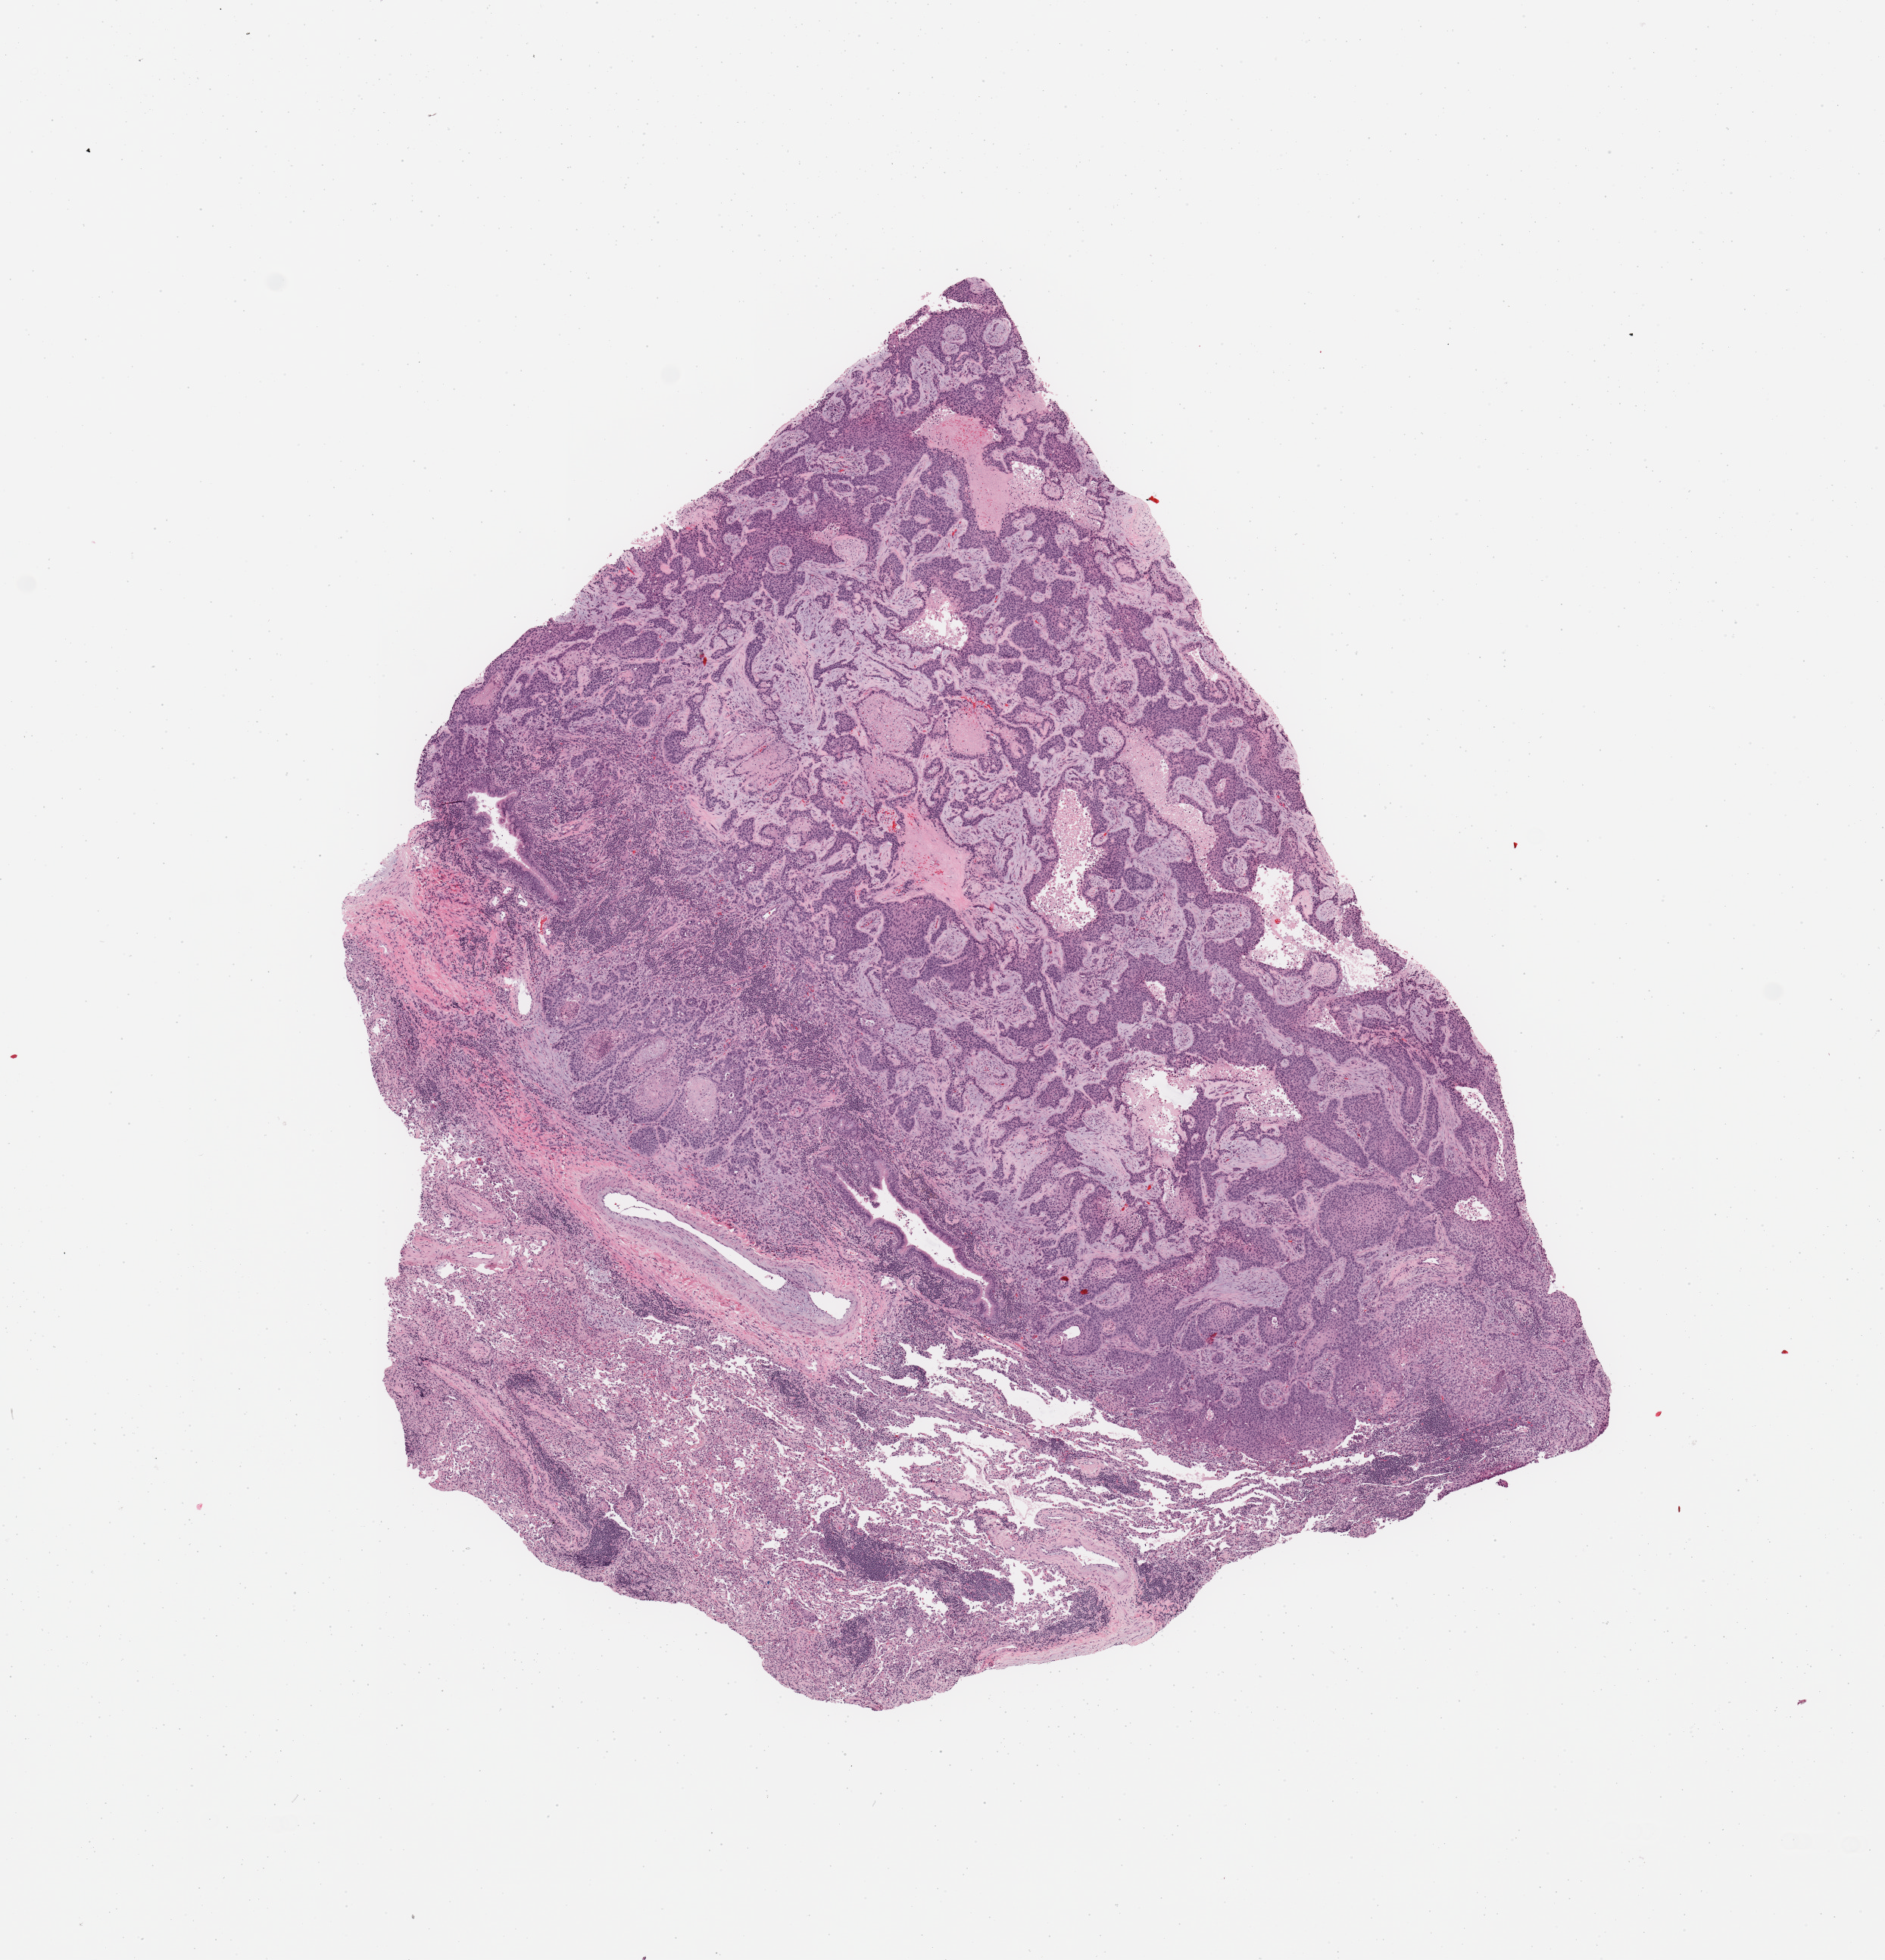
H&E whole-slide image — low-resolution overview of the scanned area, about 9.8 x 10.2 mm (acquisition: 20x scan); tumour tissue sample, lung. 75-year-old female patient. Histologic grade: G2 (moderately differentiated).
AJCC pathologic stage: IB. Primary tumour site (as recorded): right lower lobe. Histologic diagnosis: Squamous cell carcinoma, NOS.